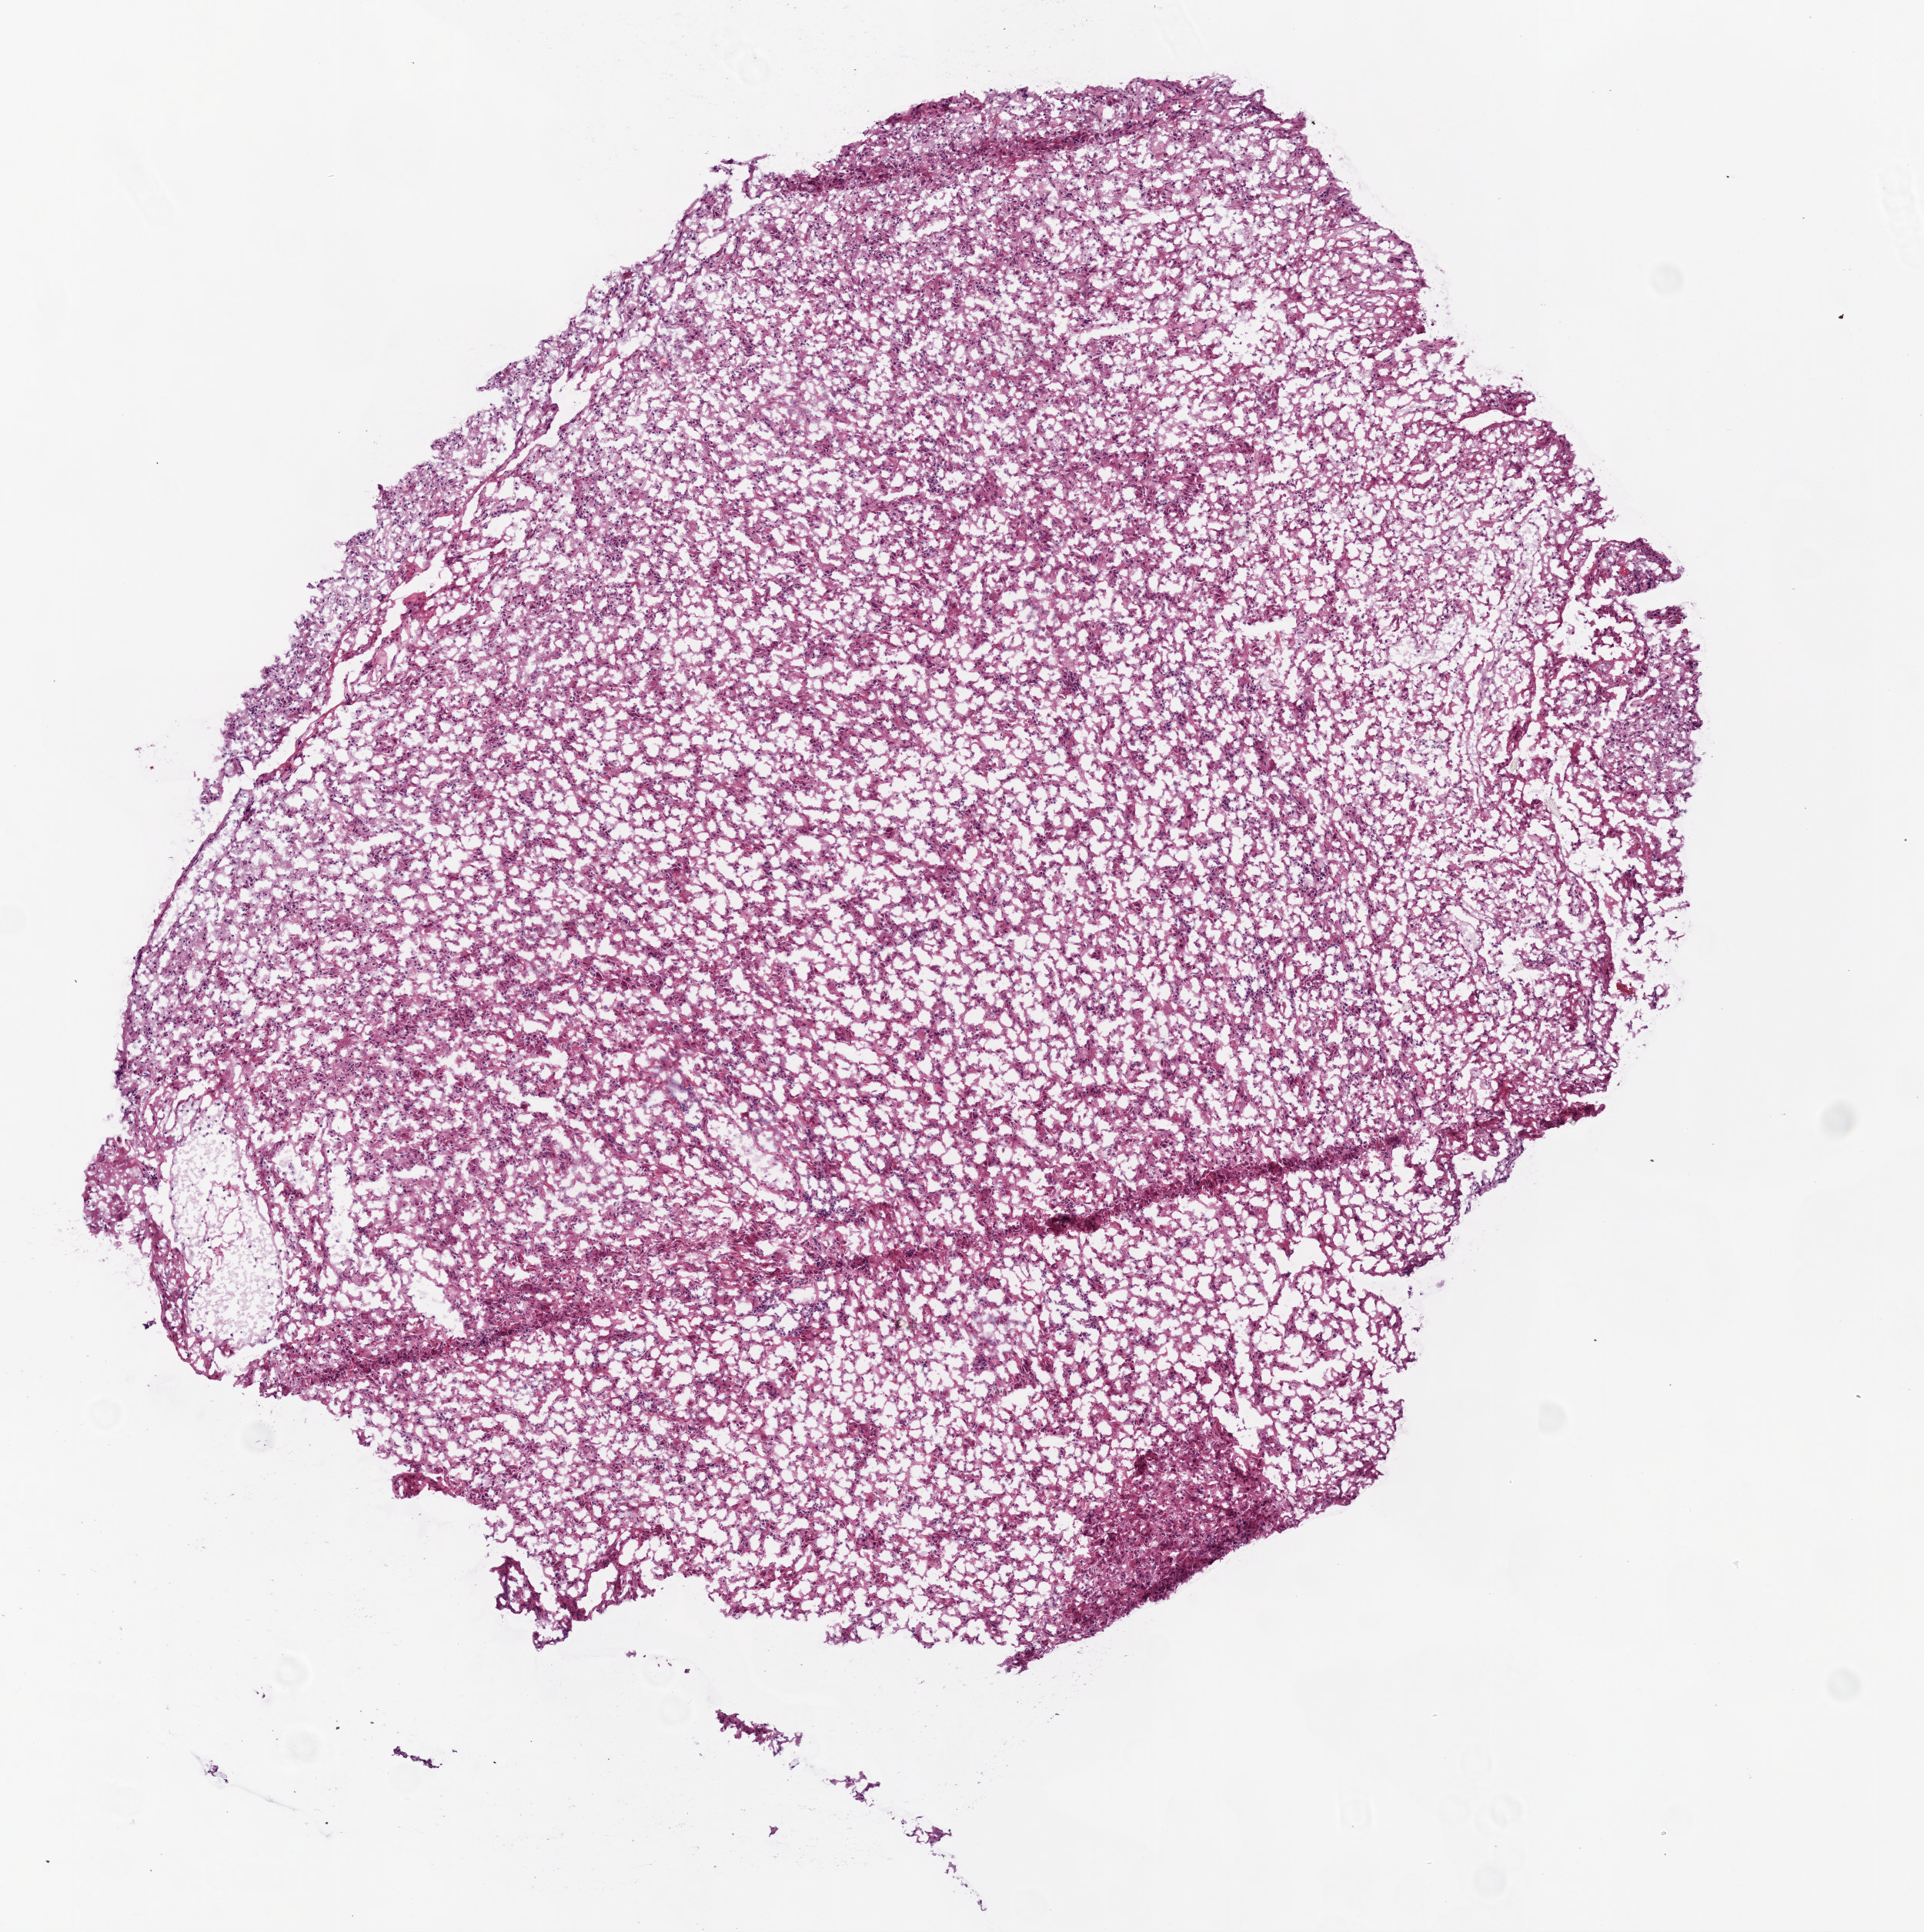
H&E whole-slide image — a low-resolution overview of the entire scanned area, about 5.0 x 5.0 mm, frozen section from the top of the tissue portion, brain, primary tumour sample. Male, age 76 years at initial diagnosis. Pathologist review of this section (percent, as recorded): tumour cells 90%, tumour nuclei 90%, normal cells 0%, stromal cells 10%, necrosis 0%.
• histologic diagnosis: Glioblastoma